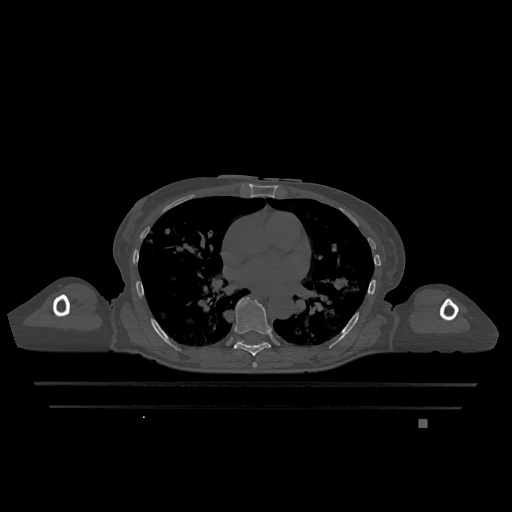
CT including the spine, one axial slice; slice 733 of 1317 in the series (ordered by position); bone window (W 1800 / L 400 HU); 512 × 512 image matrix, field of view 500 × 500 mm. Patient: female, 74 years. From the clinical record (not read from this slice): primary cancer: lung; vertebrae with lytic lesions (as recorded): T1, T4, T5, T6, L4, L5.
Annotated regions visible in this slice (semi-automatic segmentation, software-assisted and operator-edited):
- T6 vertebra: box from (x=252, y=362) to (x=257, y=368) px
- T7 vertebra: (x=234, y=297)–(x=271, y=356)
- T9 vertebra: (x=237, y=340)–(x=239, y=342)